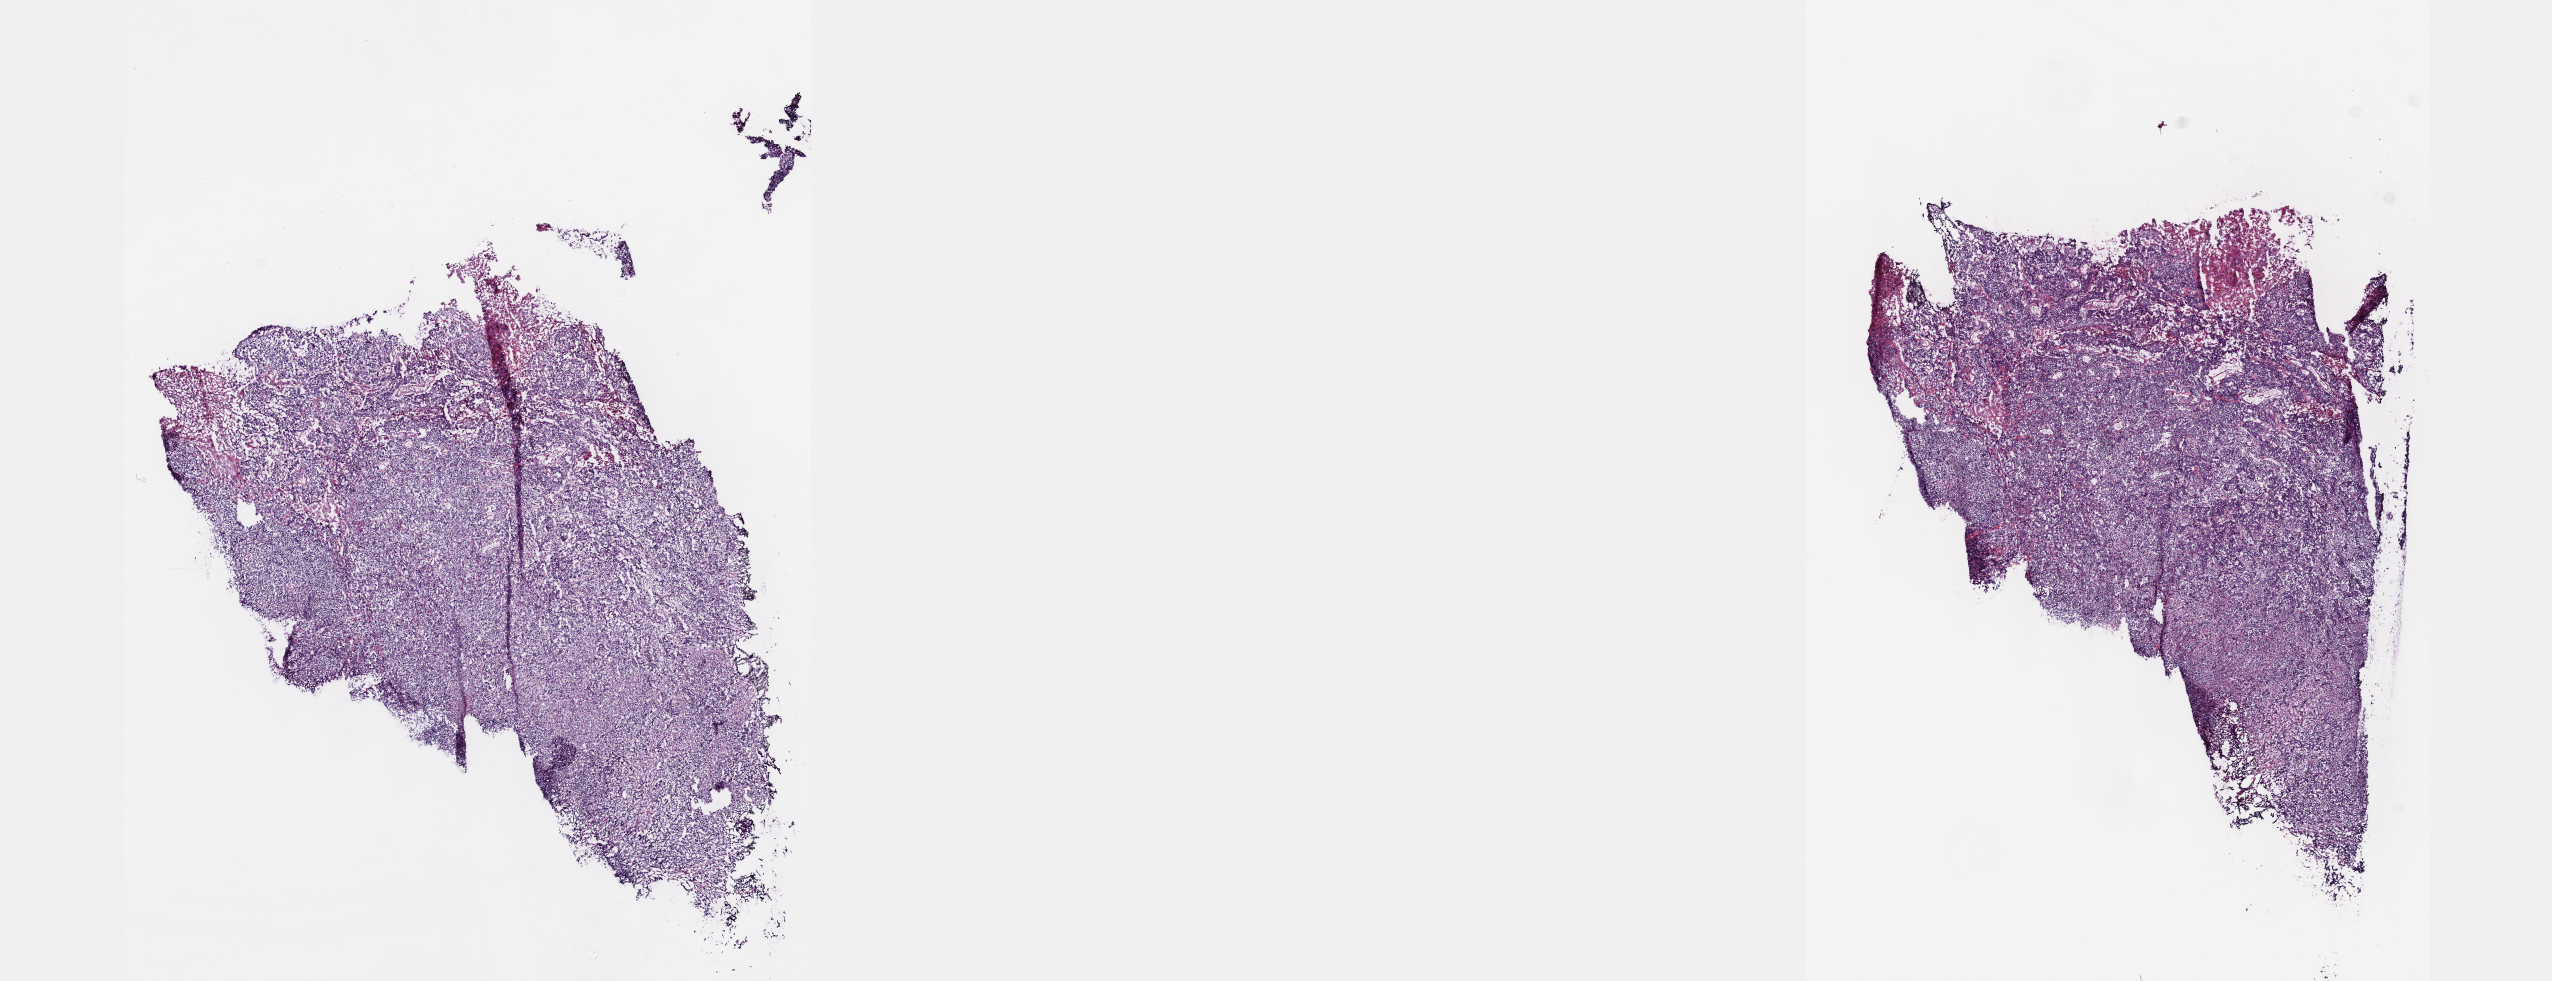
H&E-stained whole-slide image, shown as a low-resolution overview of the whole scanned area (about 20.6 x 7.9 mm, slide scanned at 40x), frozen section, primary tumour sample from the bladder. Patient: female, age at initial diagnosis 70 years. Histologic grade: high grade. Slide review estimates, as recorded: tumour cells 70%, tumour nuclei 80%, normal cells 0%, stromal cells 30%, necrosis 0%. Inflammatory infiltration, as recorded: lymphocyte infiltration 0%, monocyte infiltration 0%, neutrophil infiltration 0%.
Histologic diagnosis: Transitional cell carcinoma (lateral wall of bladder). AJCC pathologic stage: III (7th edition).